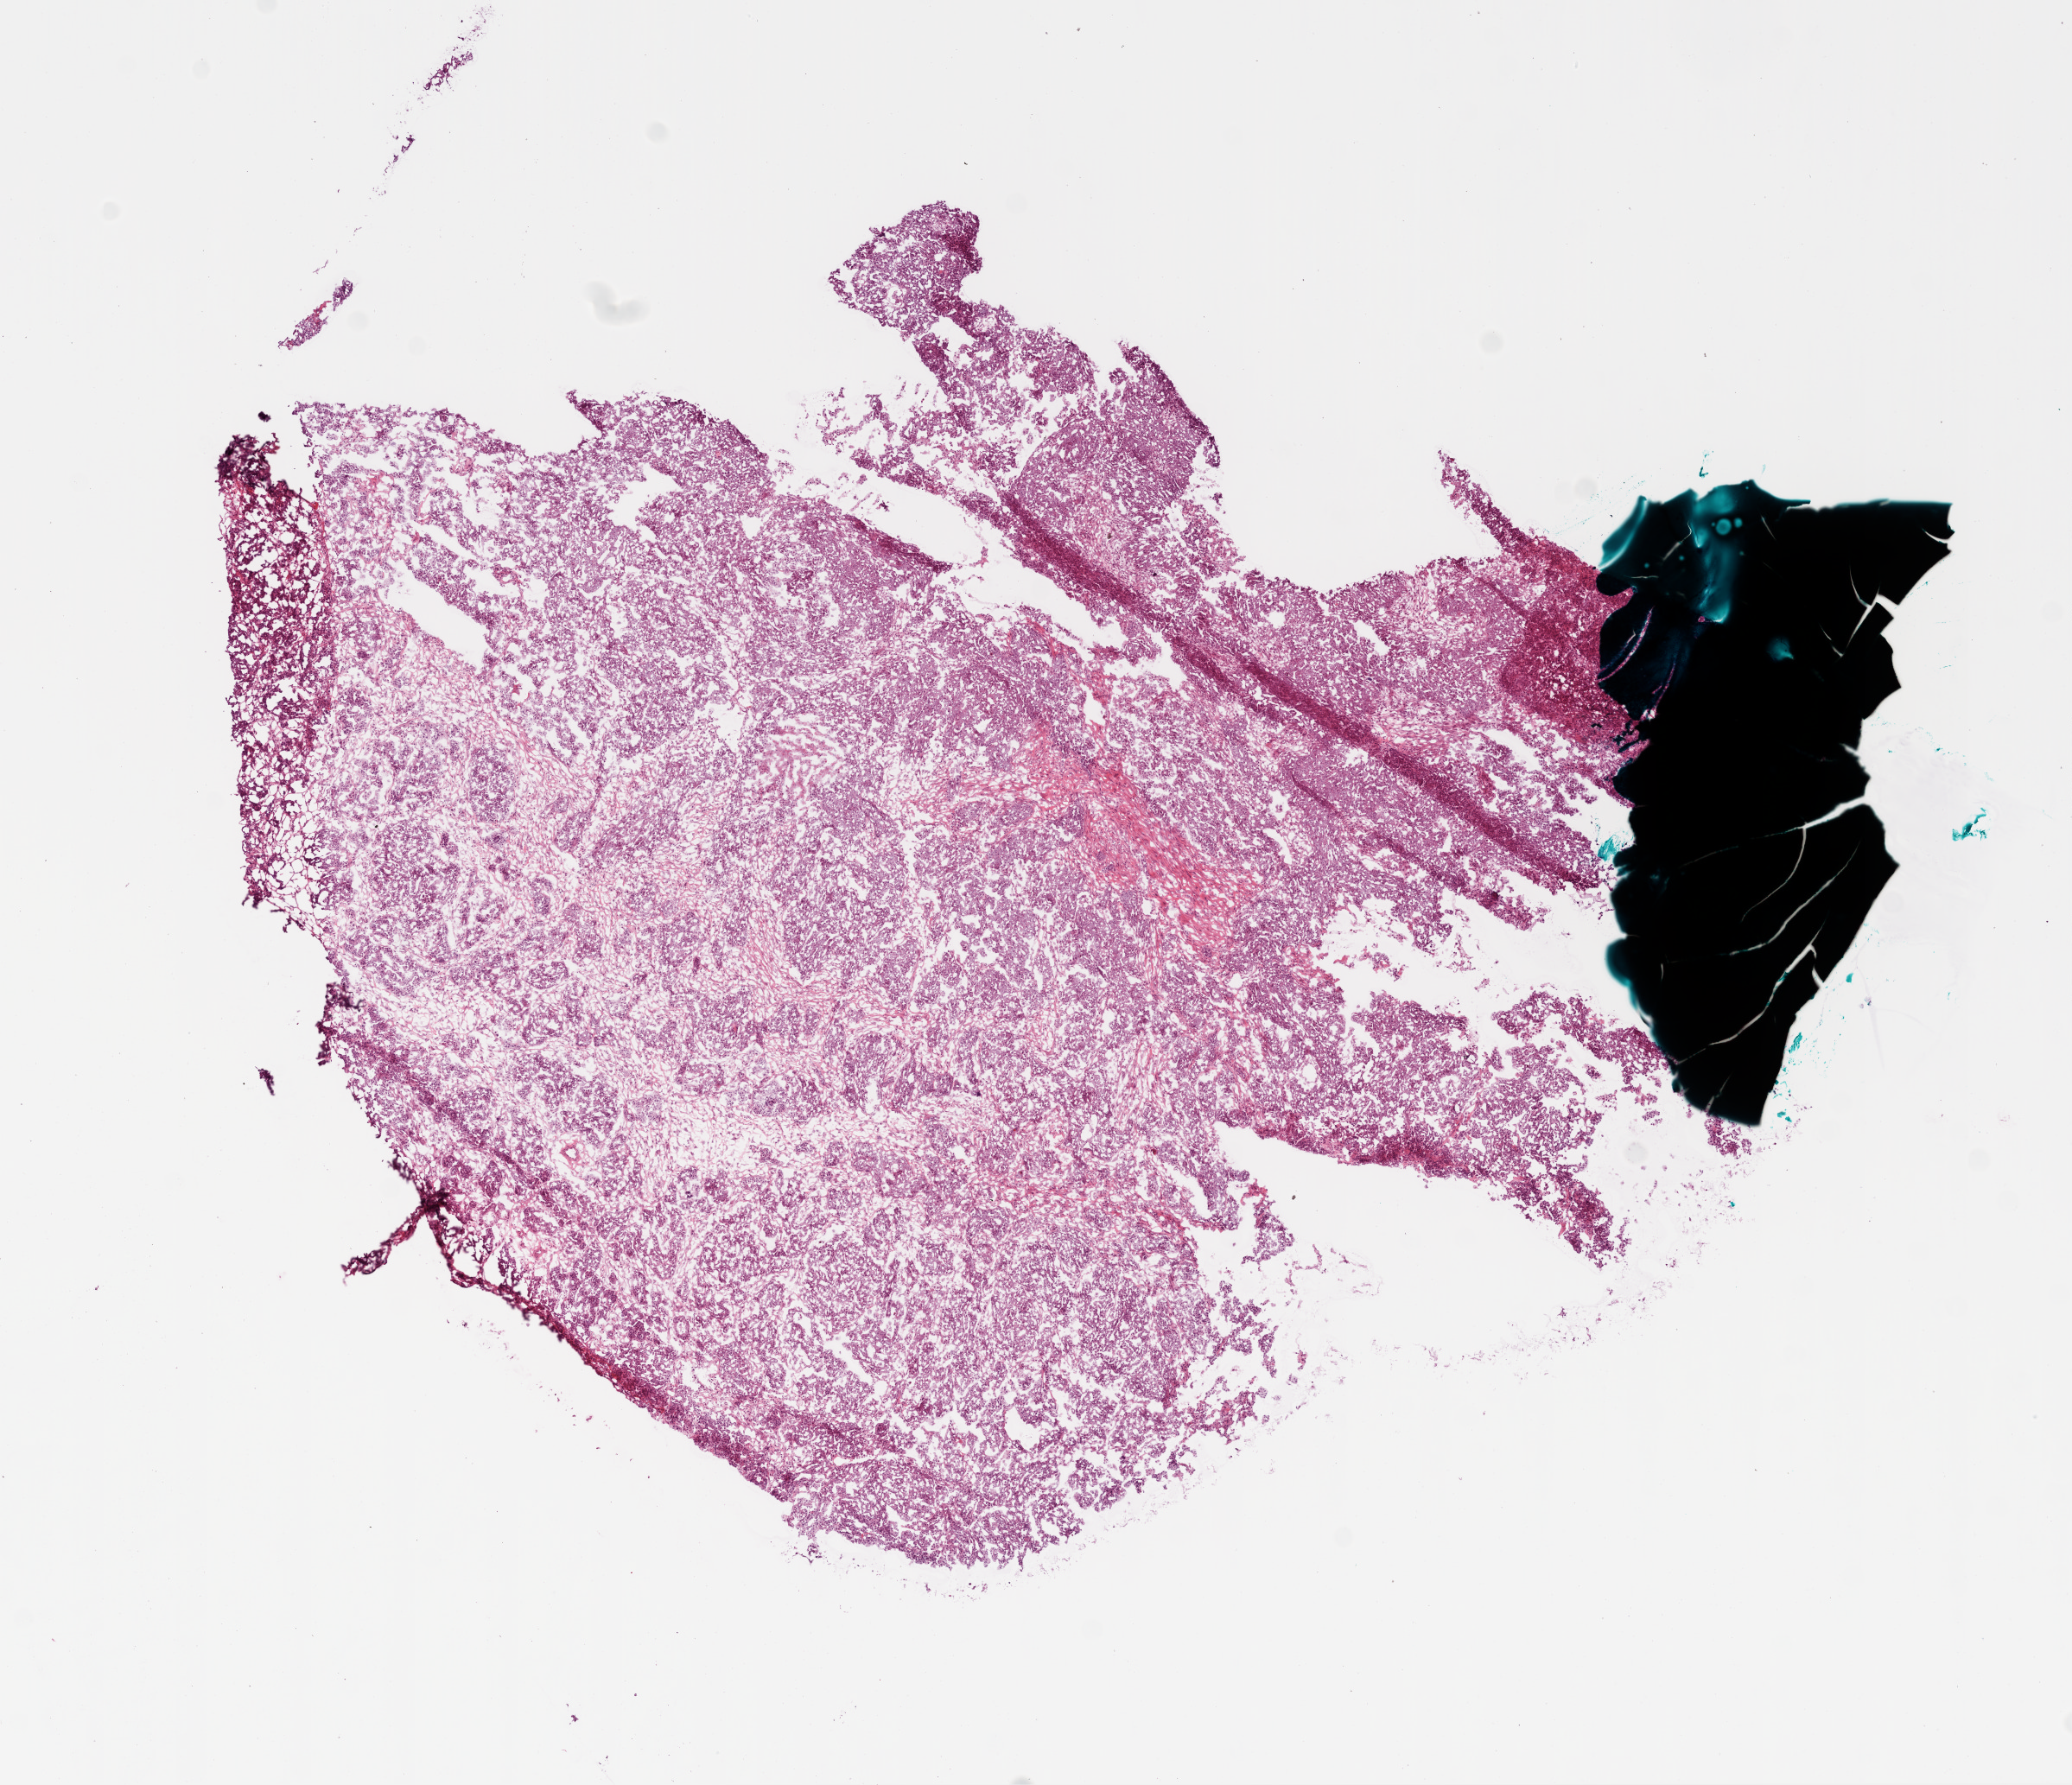
Whole-slide histology image, Hematoxylin and eosin (H&E) stained, shown as a low-resolution overview of the whole scanned area (about 9.7 x 8.3 mm). Frozen section from the bottom of the tissue portion. Ovary, primary tumour sample. Patient: female, age at initial diagnosis 48 years.
Pathologic diagnosis: Serous cystadenocarcinoma, NOS.